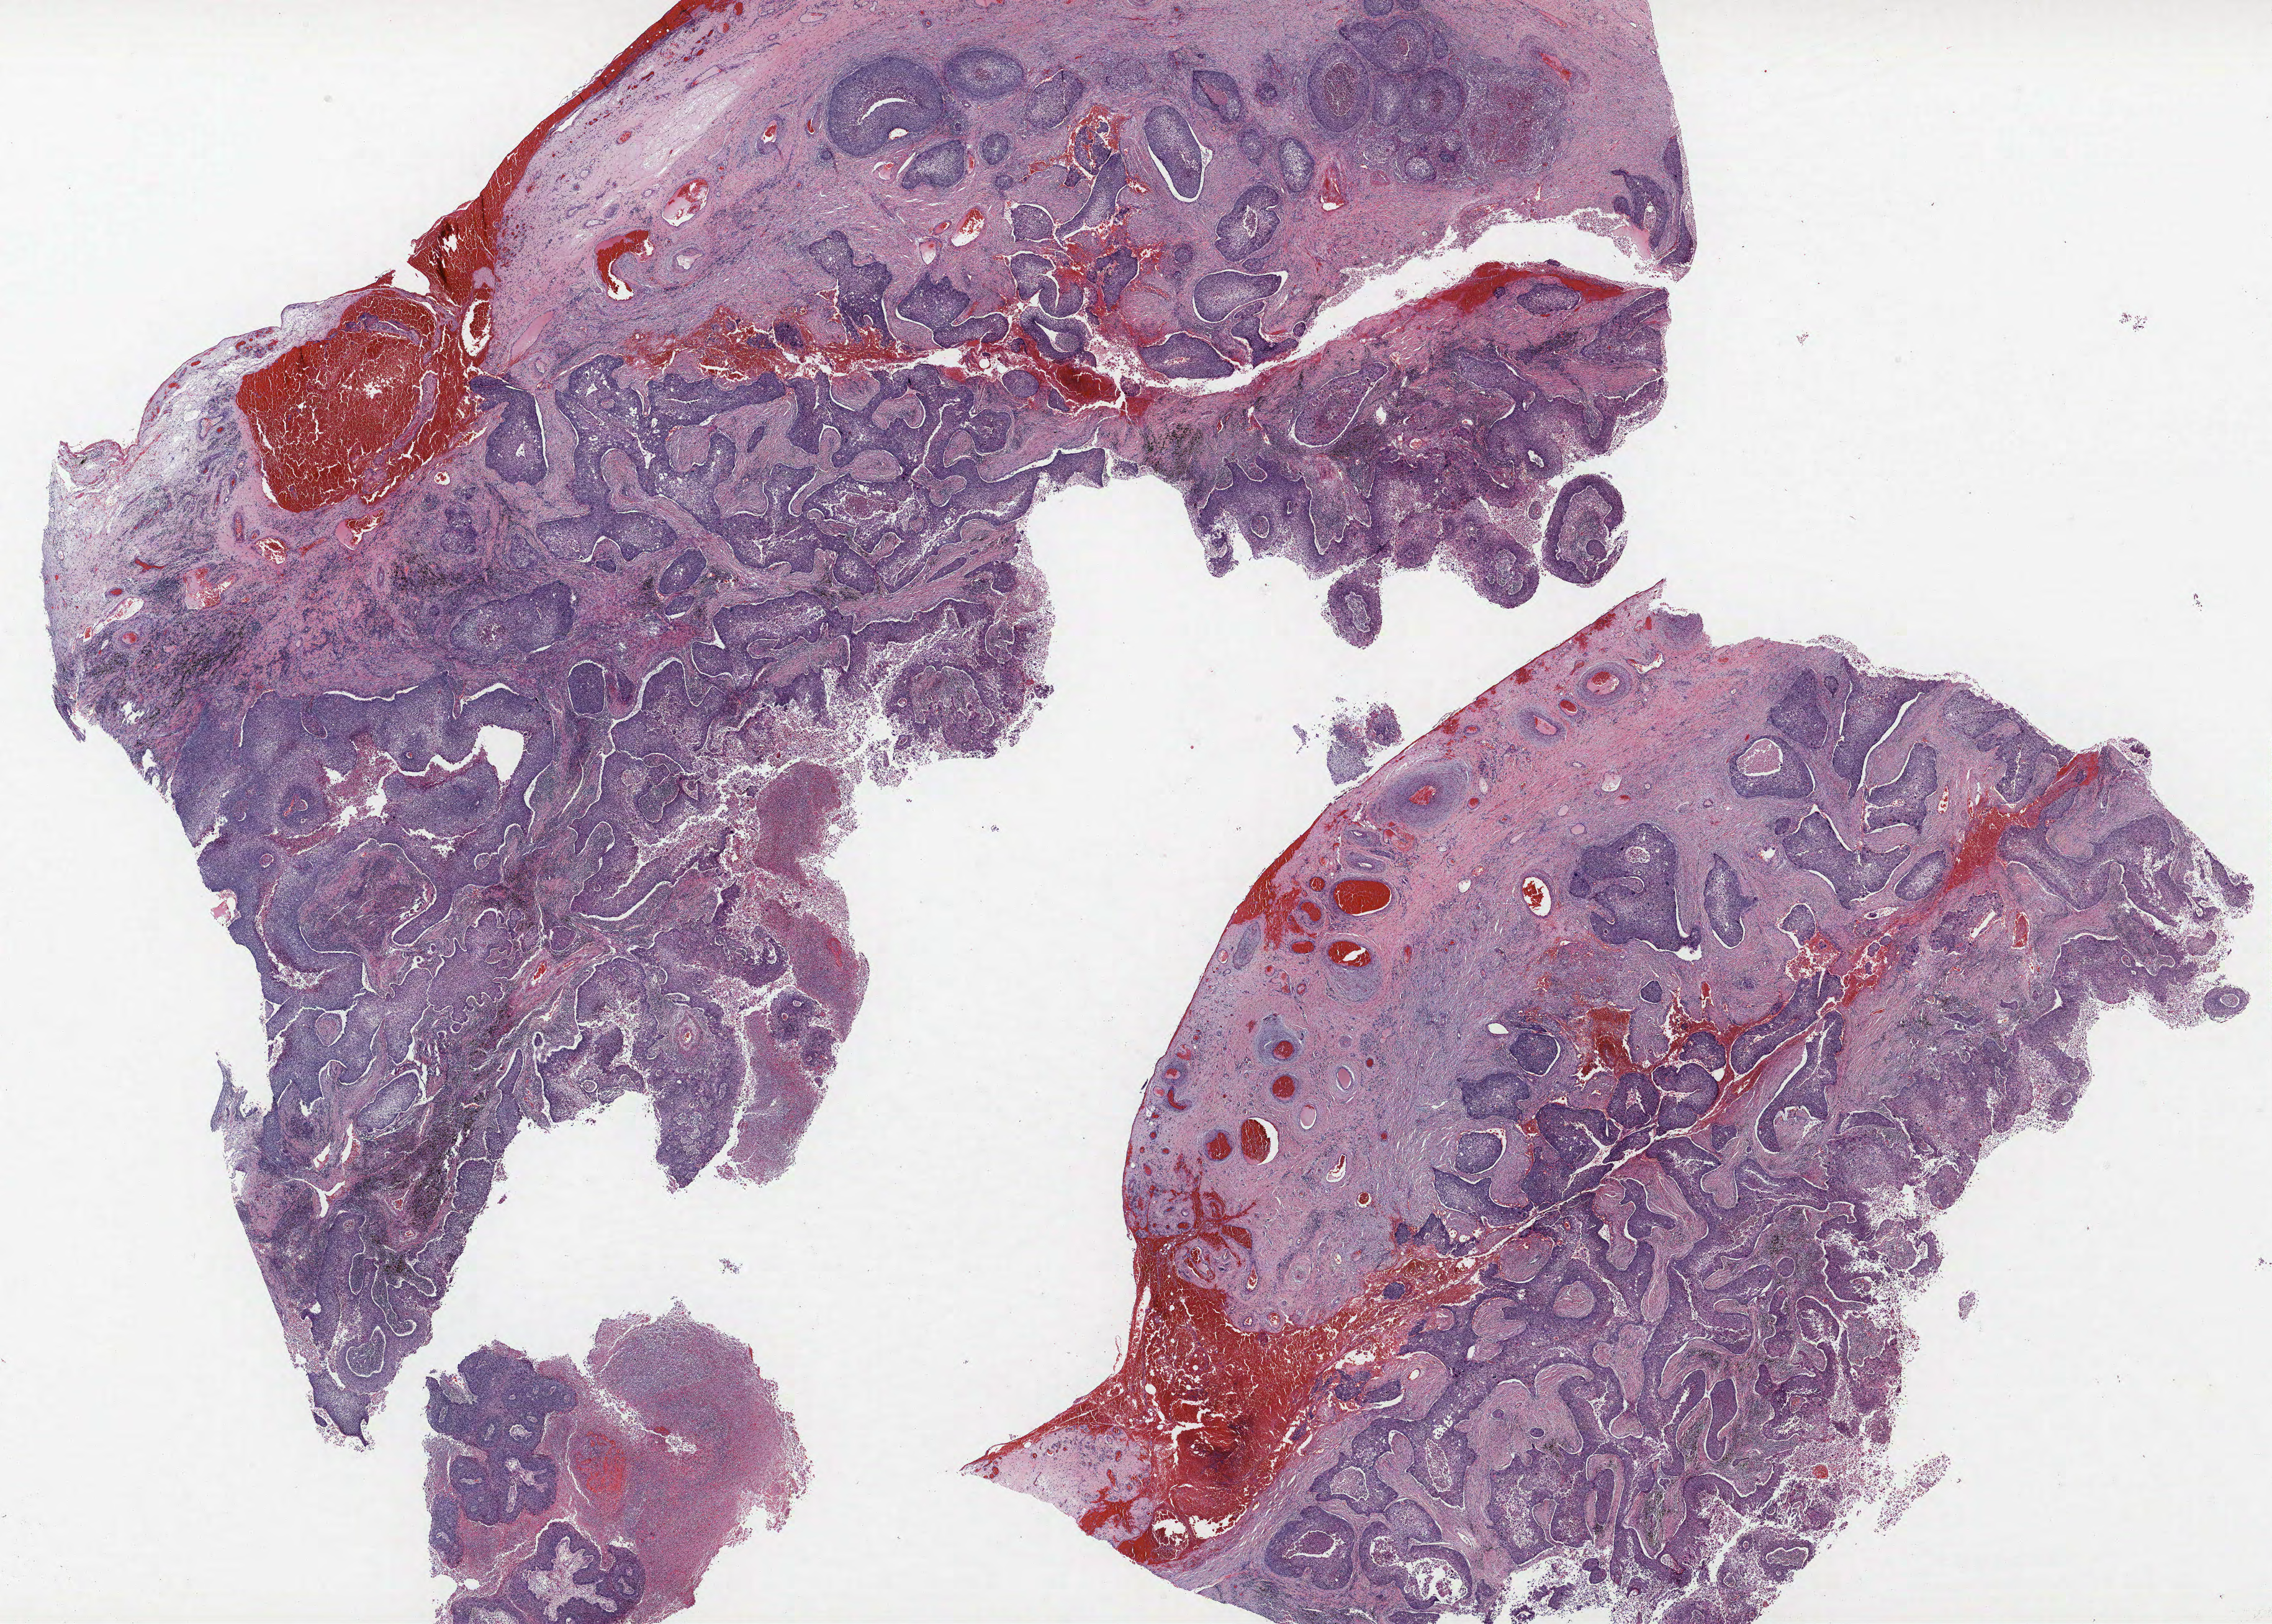
H&E-stained whole-slide image, whole scanned area (about 29.3 x 20.9 mm, slide scanned at 40x) shown as a low-resolution overview. Formalin-fixed paraffin-embedded (FFPE) section. Lung. Male patient, aged 71 at enrolment. Former smoker at enrolment. Grade: moderately differentiated (G2).
- tumour size (pathology): 53 mm
- primary tumour location (clinical record): right lower lobe
- stage (AJCC 6th edition): IB
- participant's lung-cancer diagnosis: Squamous cell carcinoma, NOS